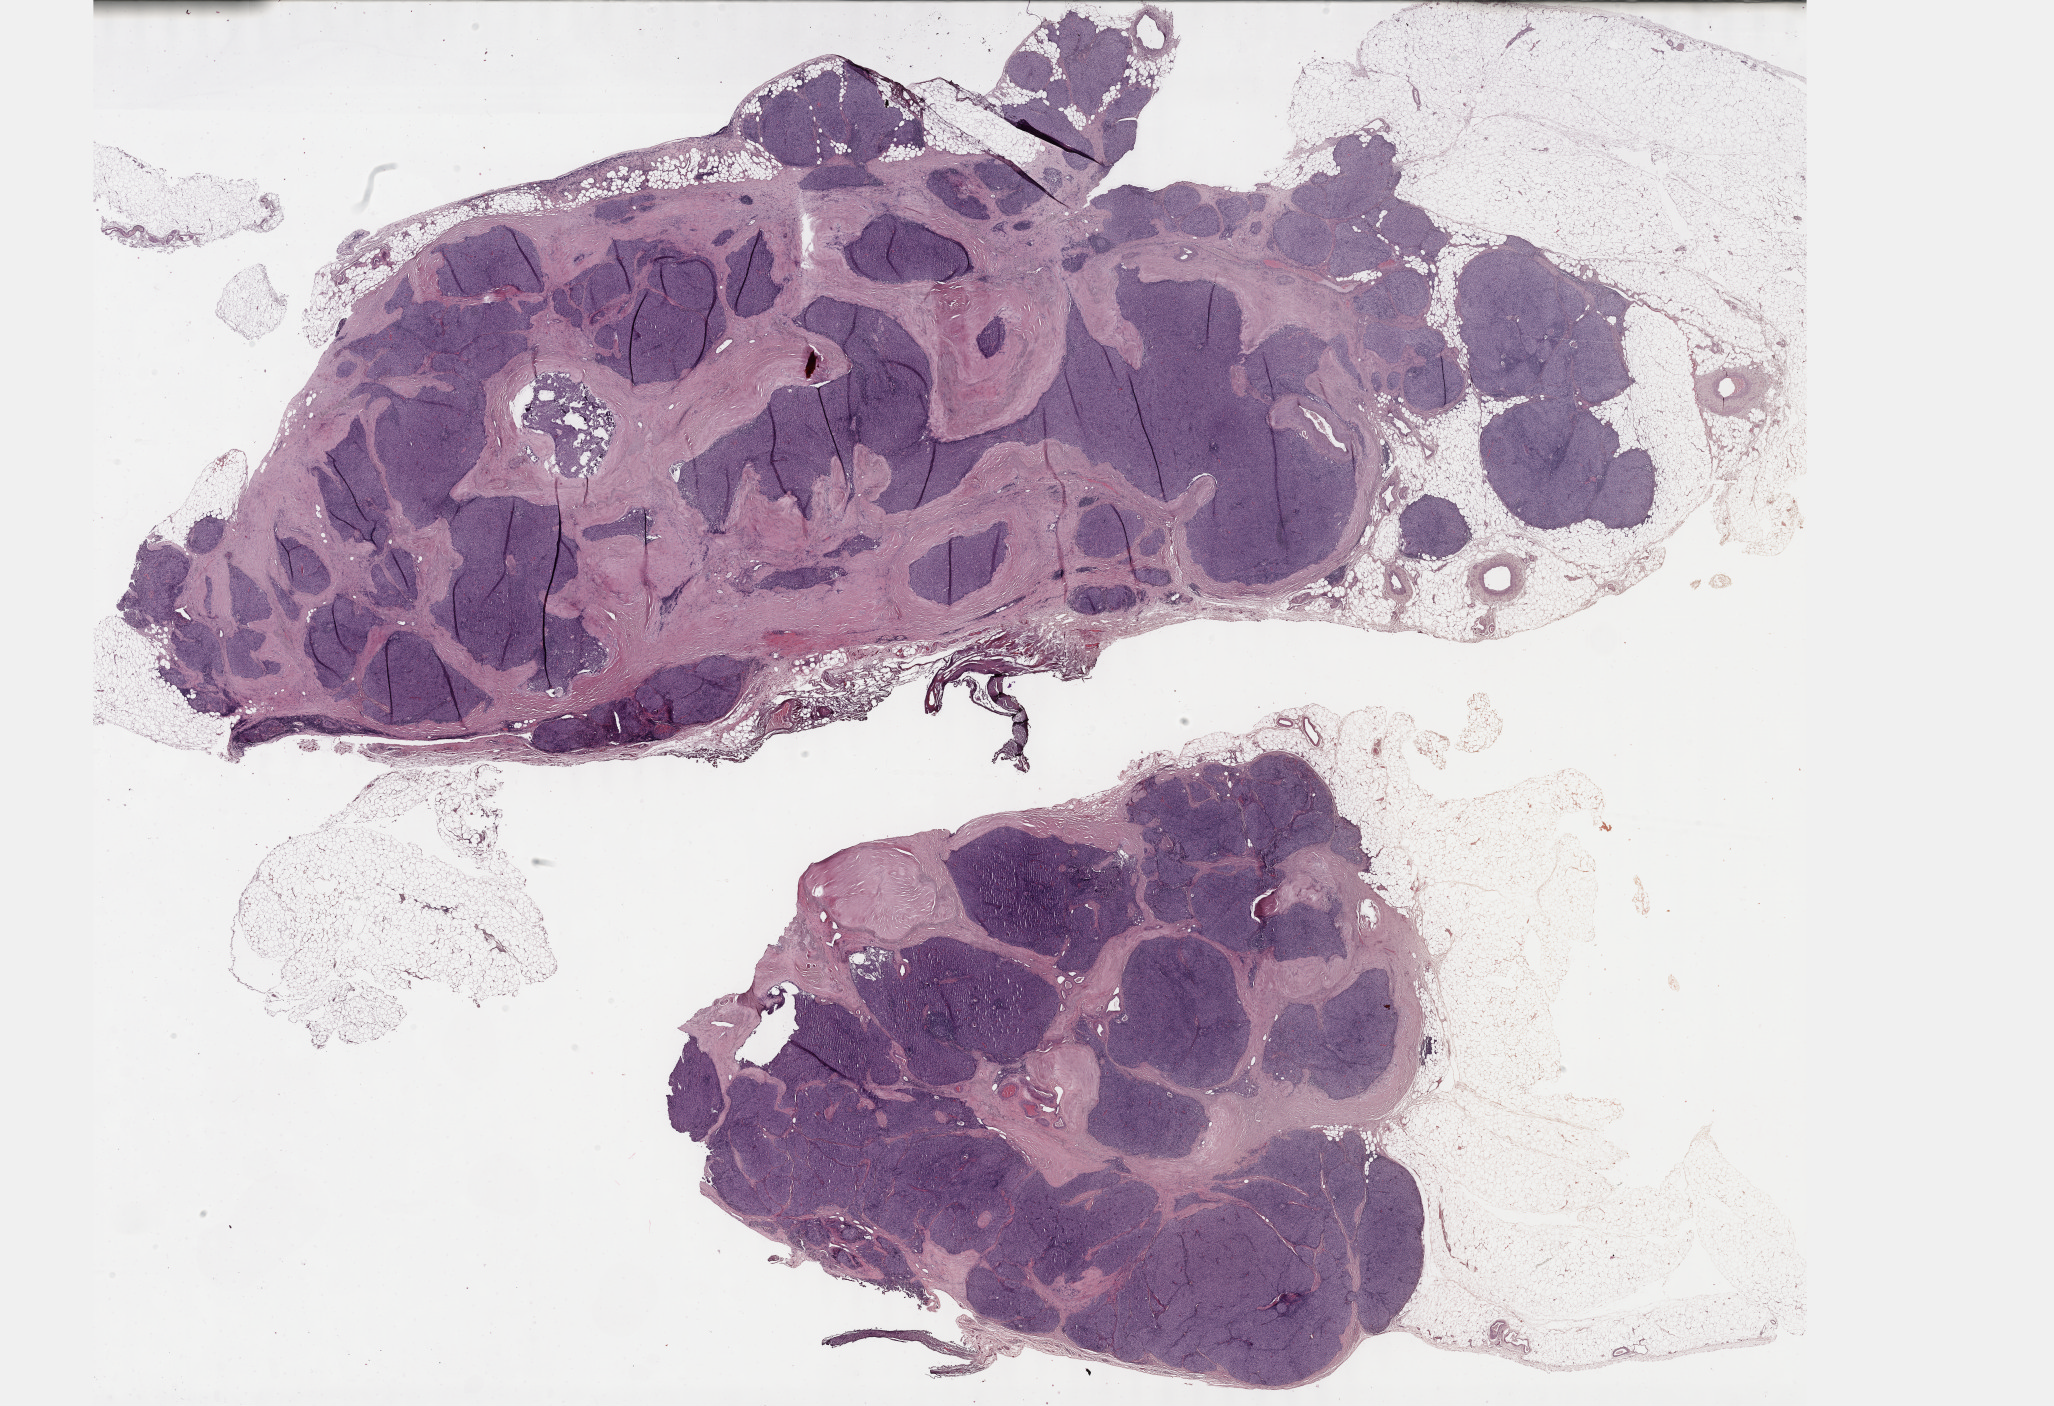
H&E-stained whole-slide image, low-resolution overview of the scanned area, about 33.2 x 22.7 mm (from a 40x scan). FFPE section. Sample: primary tumour, thymus. Male, age 62 years at initial diagnosis.
• diagnosis: Thymoma, type B3, malignant (anterior mediastinum)